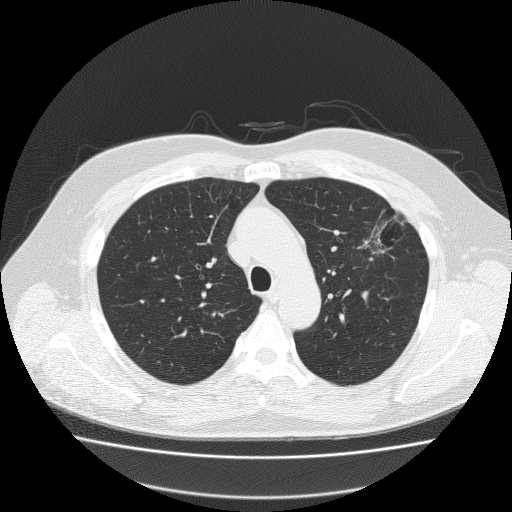
Low-dose screening chest CT, axial slice, first (baseline) screen, lung window (W 1500 / L -600 HU), lung (sharp) reconstruction kernel (FC51). Male, age 62 years at enrolment.
Expert-annotated lung lesion, bounding box (x1, y1, x2, y2) in pixels: (356, 200, 424, 261). The exam's reader record, not a measurement of the box and not confirmed to be the same lesion: non-calcified nodule or mass ≥4 mm, left upper lobe, 18 × 8 mm, spiculated (stellate) margins, soft tissue attenuation. Official screen result: positive, change unspecified: nodule(s) >= 4 mm or enlarging nodule(s), mass(es), or other non-specific abnormalities suspicious for lung cancer. Participant outcome: lung cancer diagnosed 49 days after this screen — bronchiolo-alveolar adenocarcinoma, NOS, left upper lobe, well differentiated (G1), stage IA (AJCC 6th edition), 25 mm at pathology.